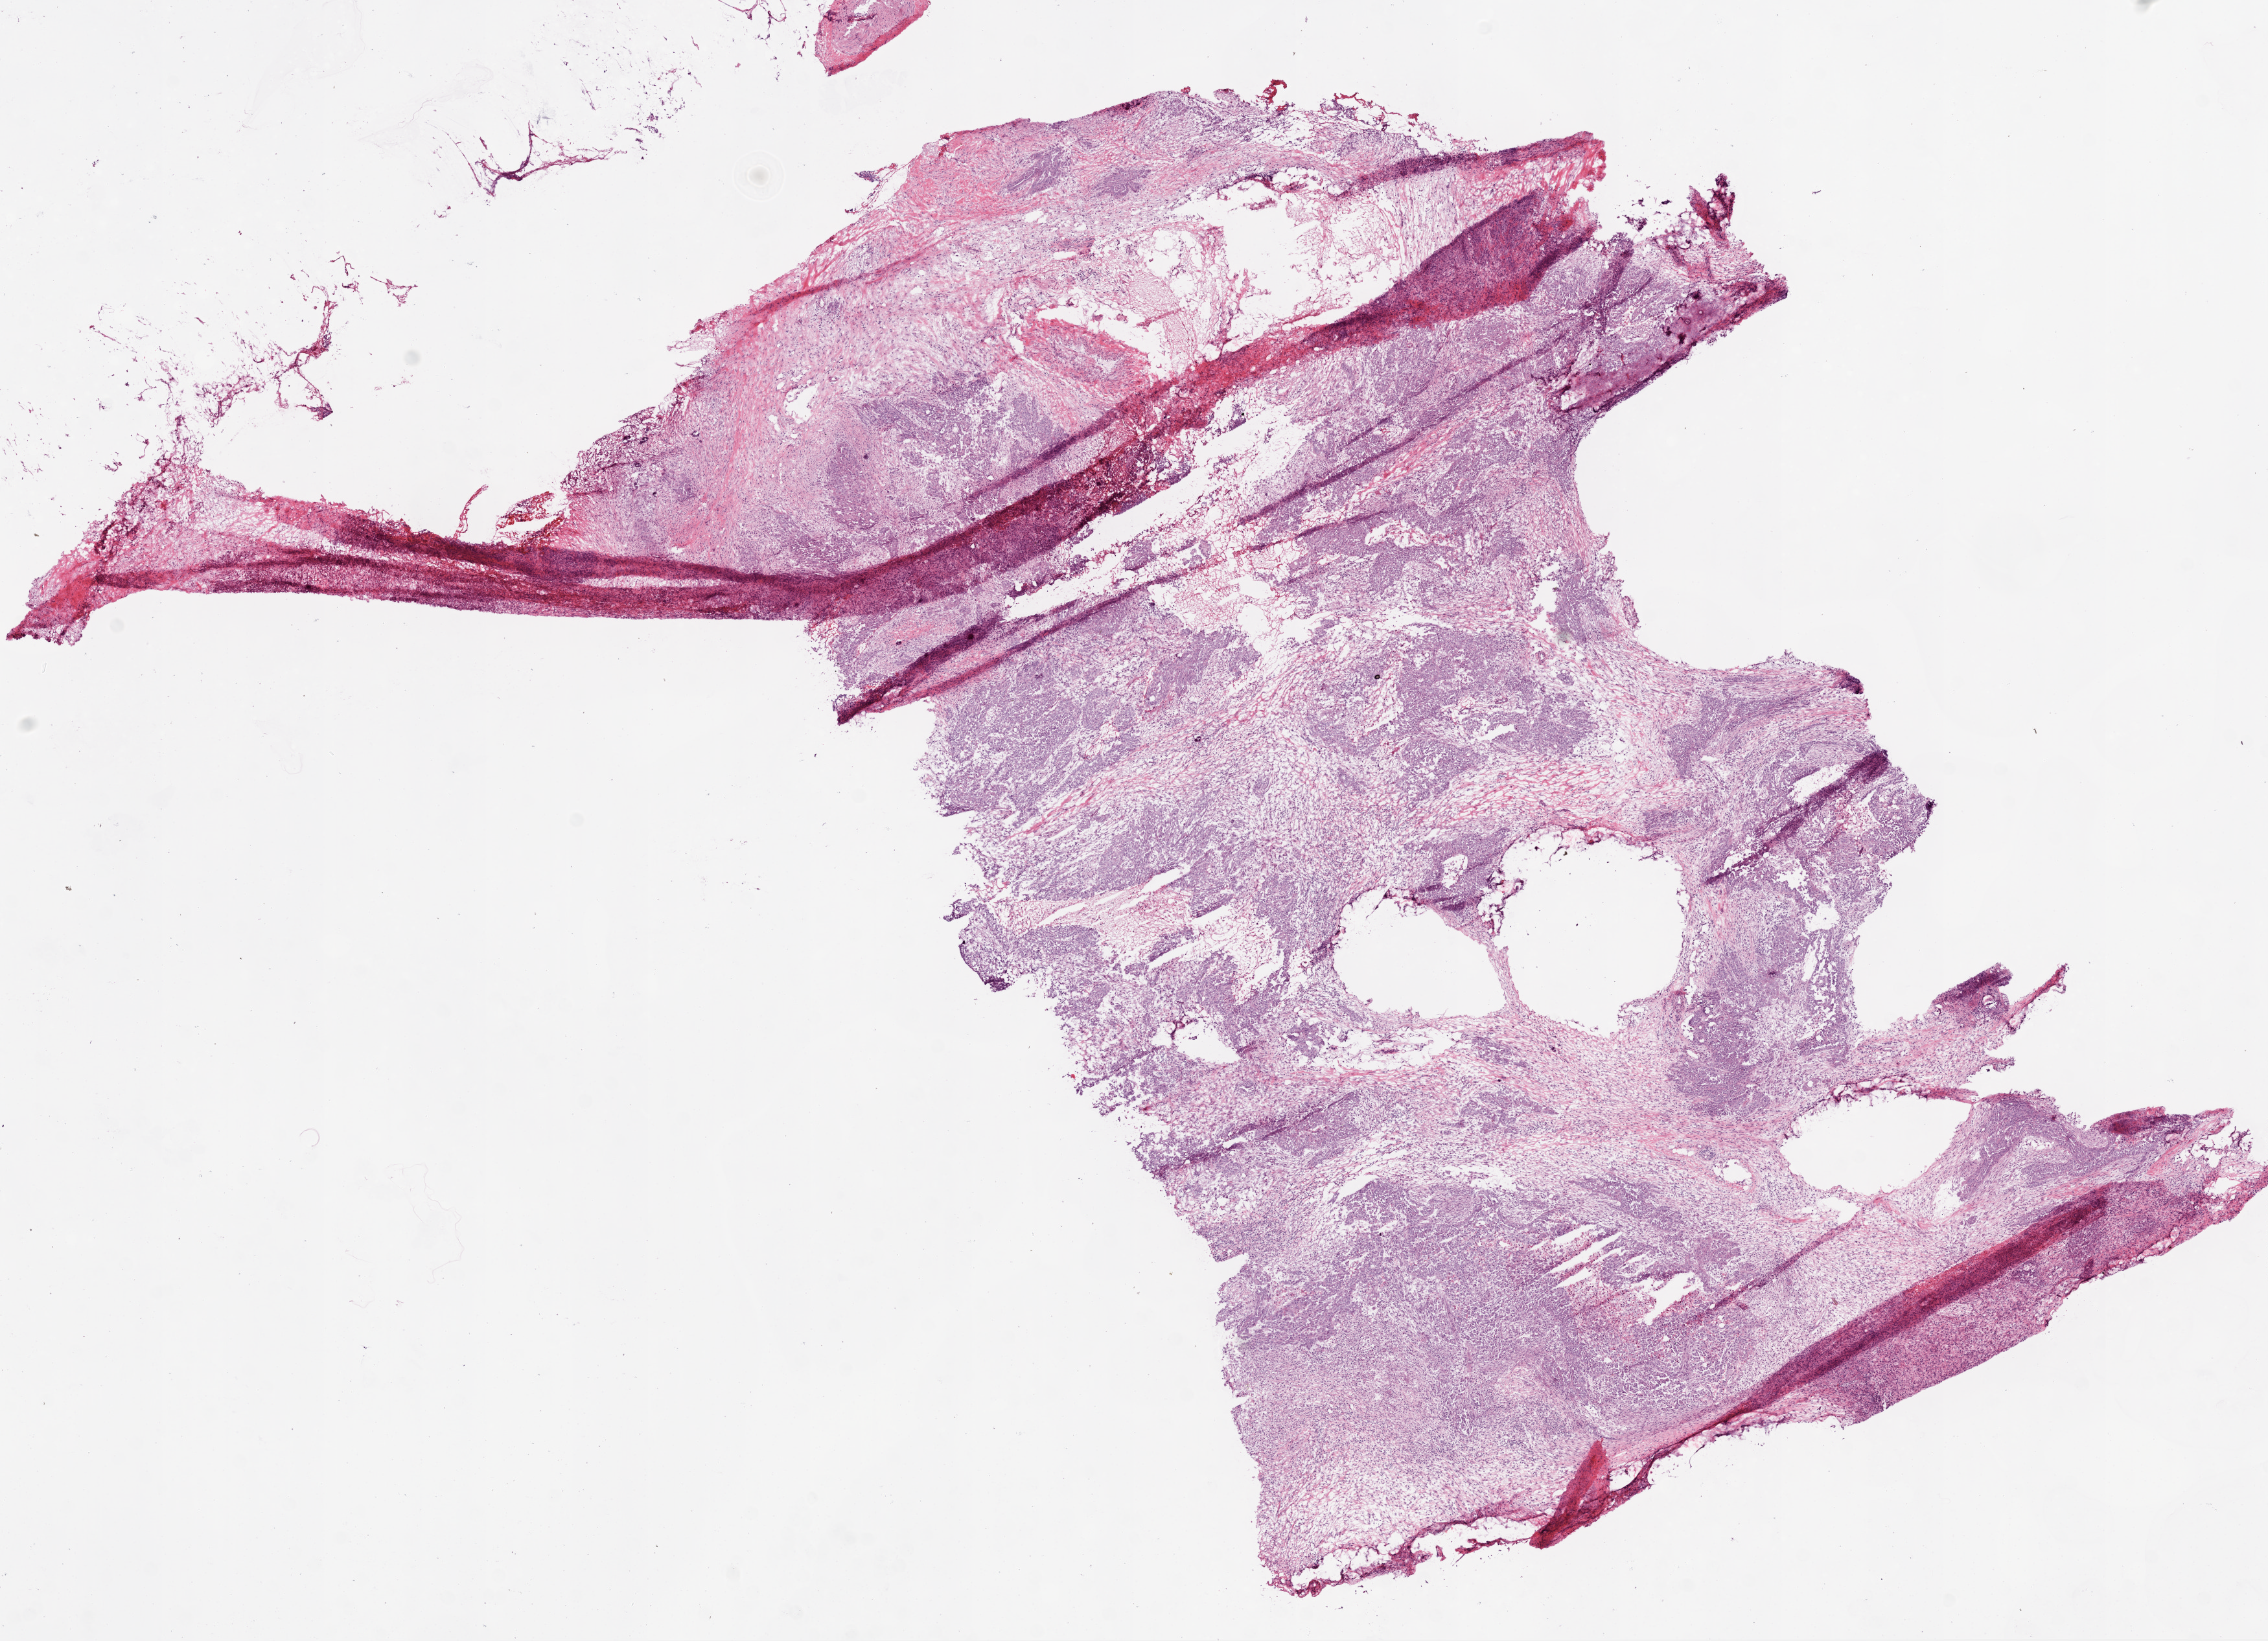
Digitized H&E-stained tissue section (whole slide) — whole scanned area (about 14.0 x 10.2 mm, slide scanned at 20x) shown as a low-resolution overview; frozen section from the bottom of the tissue portion; sample: primary tumour, ovary. Female patient; age at initial diagnosis 65 years. Histologic grade: G3 (poorly differentiated). Pathologist review of this section (percent, as recorded): tumour cells 65%, tumour nuclei 75%, normal cells 0%, stromal cells 30%, necrosis 5%.
- laterality: right
- pathologic diagnosis: Serous cystadenocarcinoma, NOS
- FIGO stage: IIIC